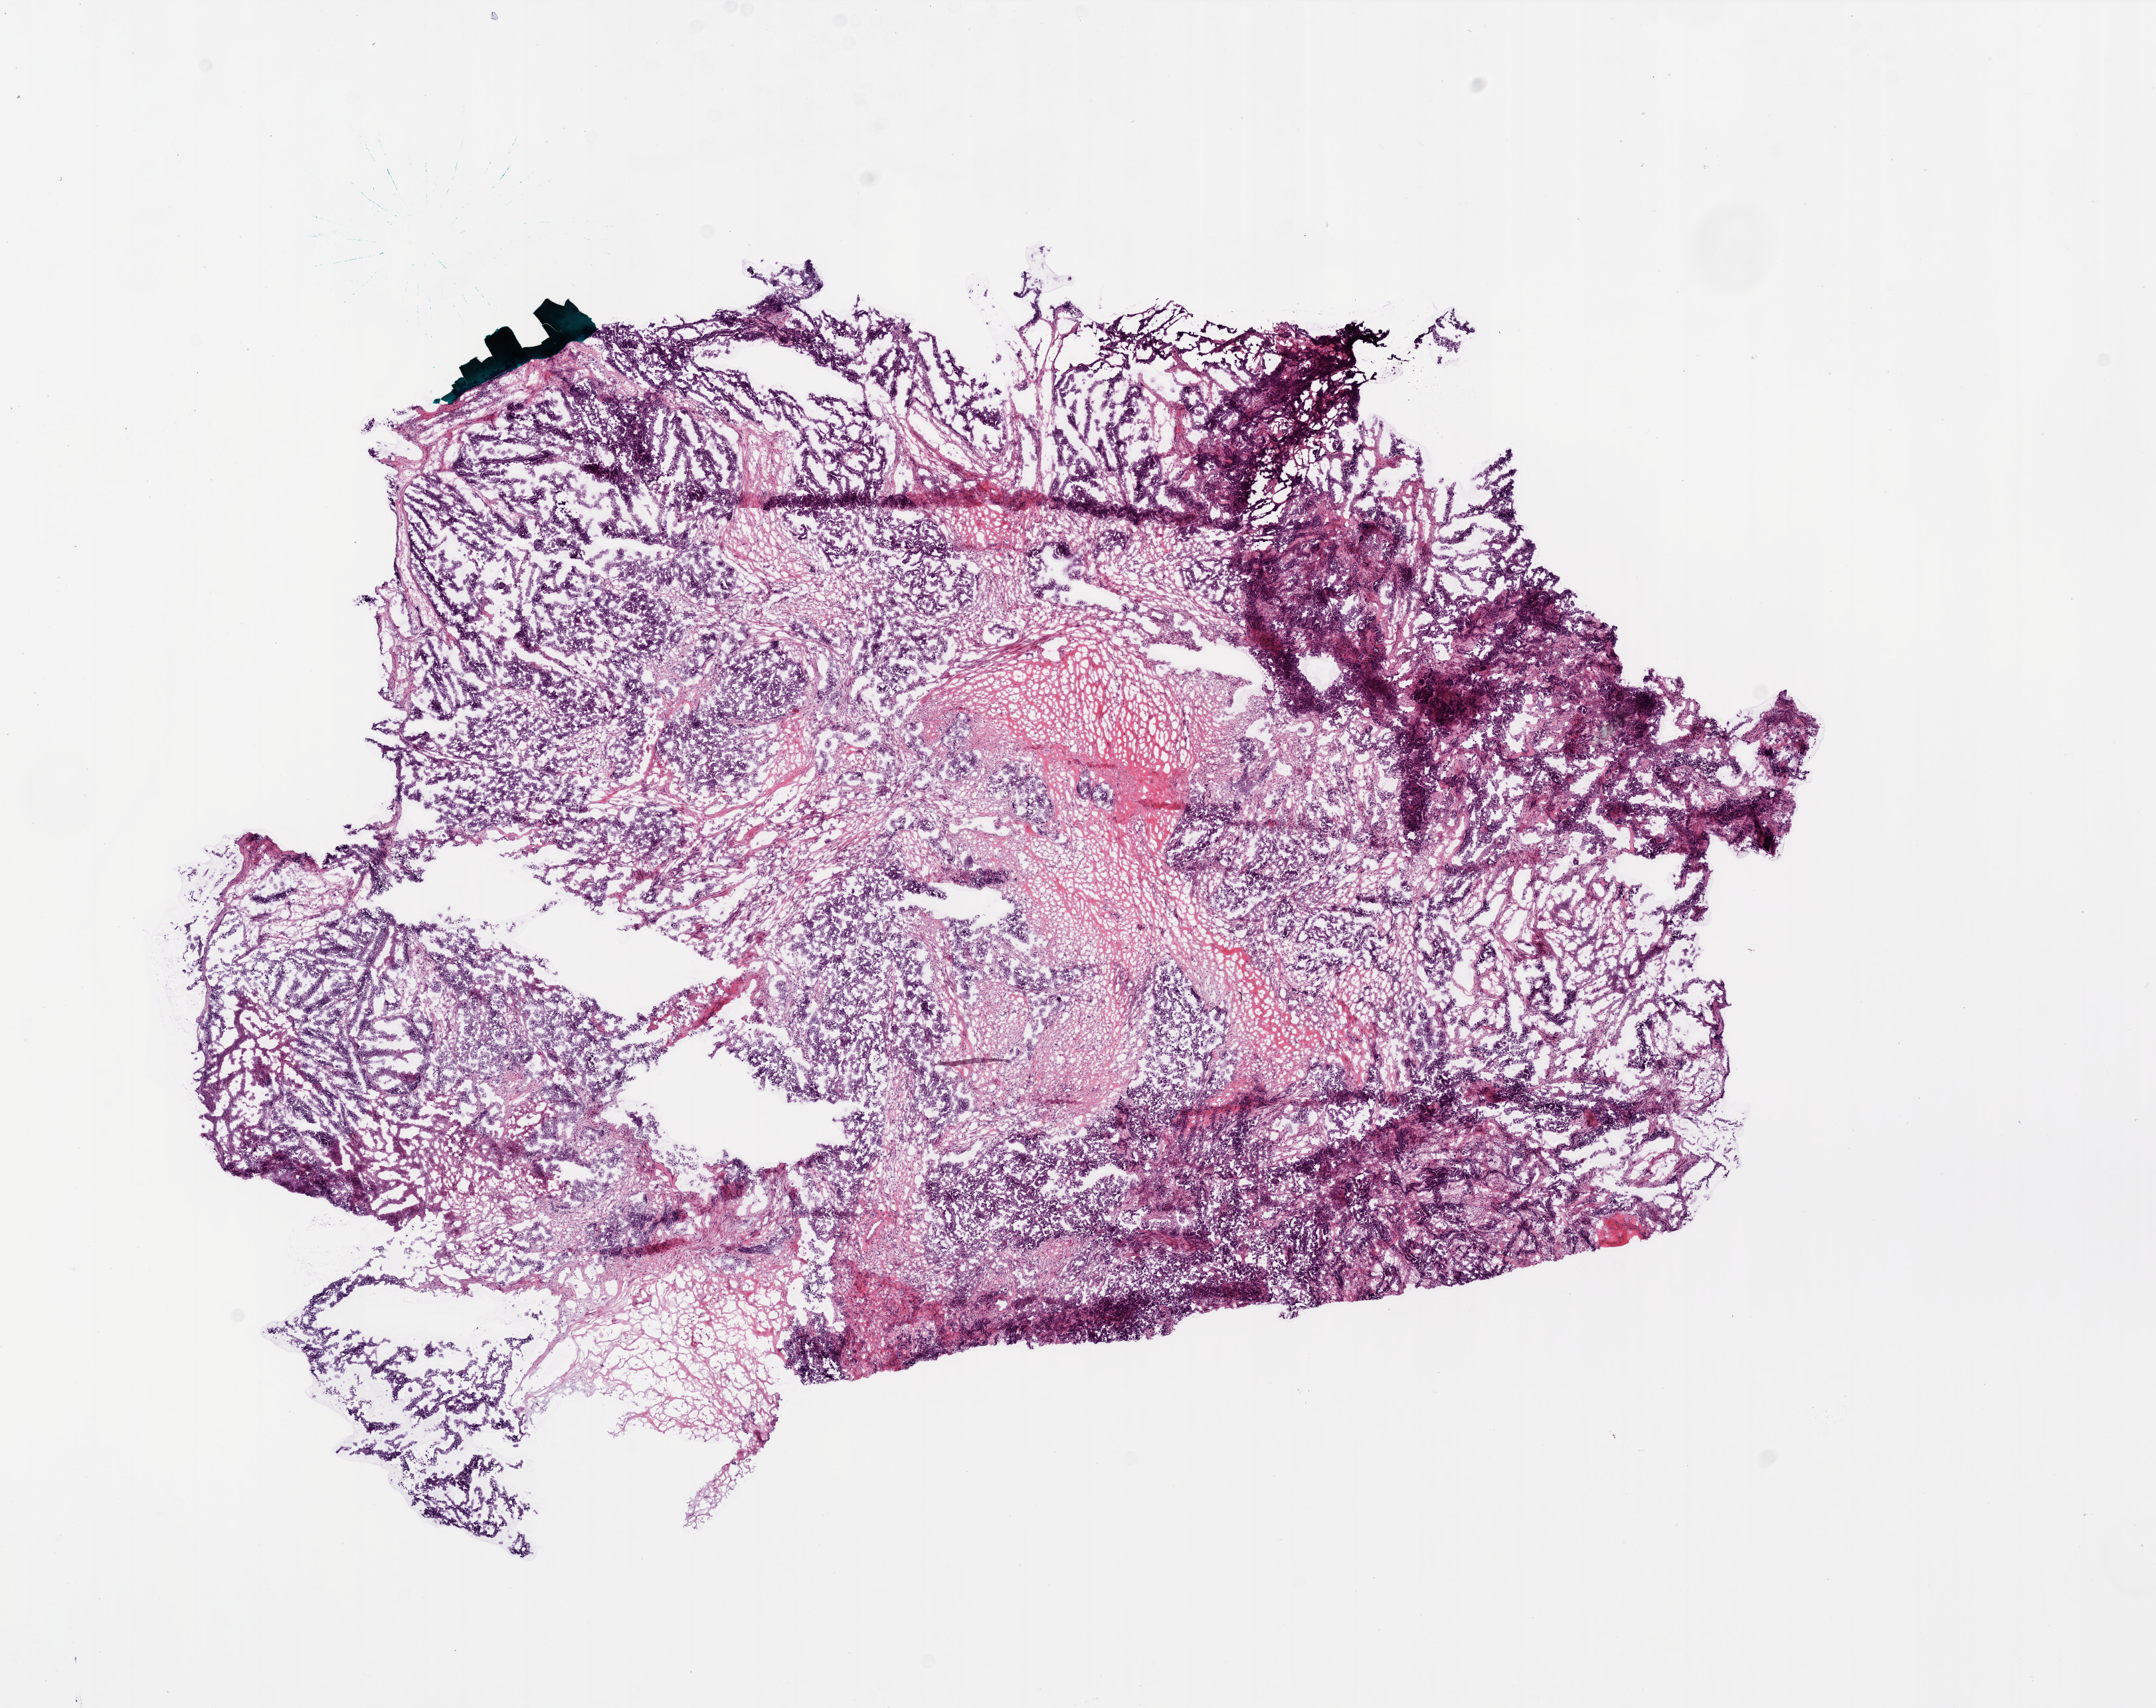
Digitized H&E-stained tissue section (whole slide), low-resolution overview of the scanned area, about 13.0 x 10.3 mm; frozen section from the bottom of the tissue portion; ovary, primary tumour sample. Female, age 45 years at initial diagnosis. Histologic grade: G3 (poorly differentiated). Slide review estimates, as recorded: tumour nuclei 90%, necrosis 10%.
• laterality: left
• pathologic diagnosis: Serous cystadenocarcinoma, NOS
• FIGO stage: IIIC